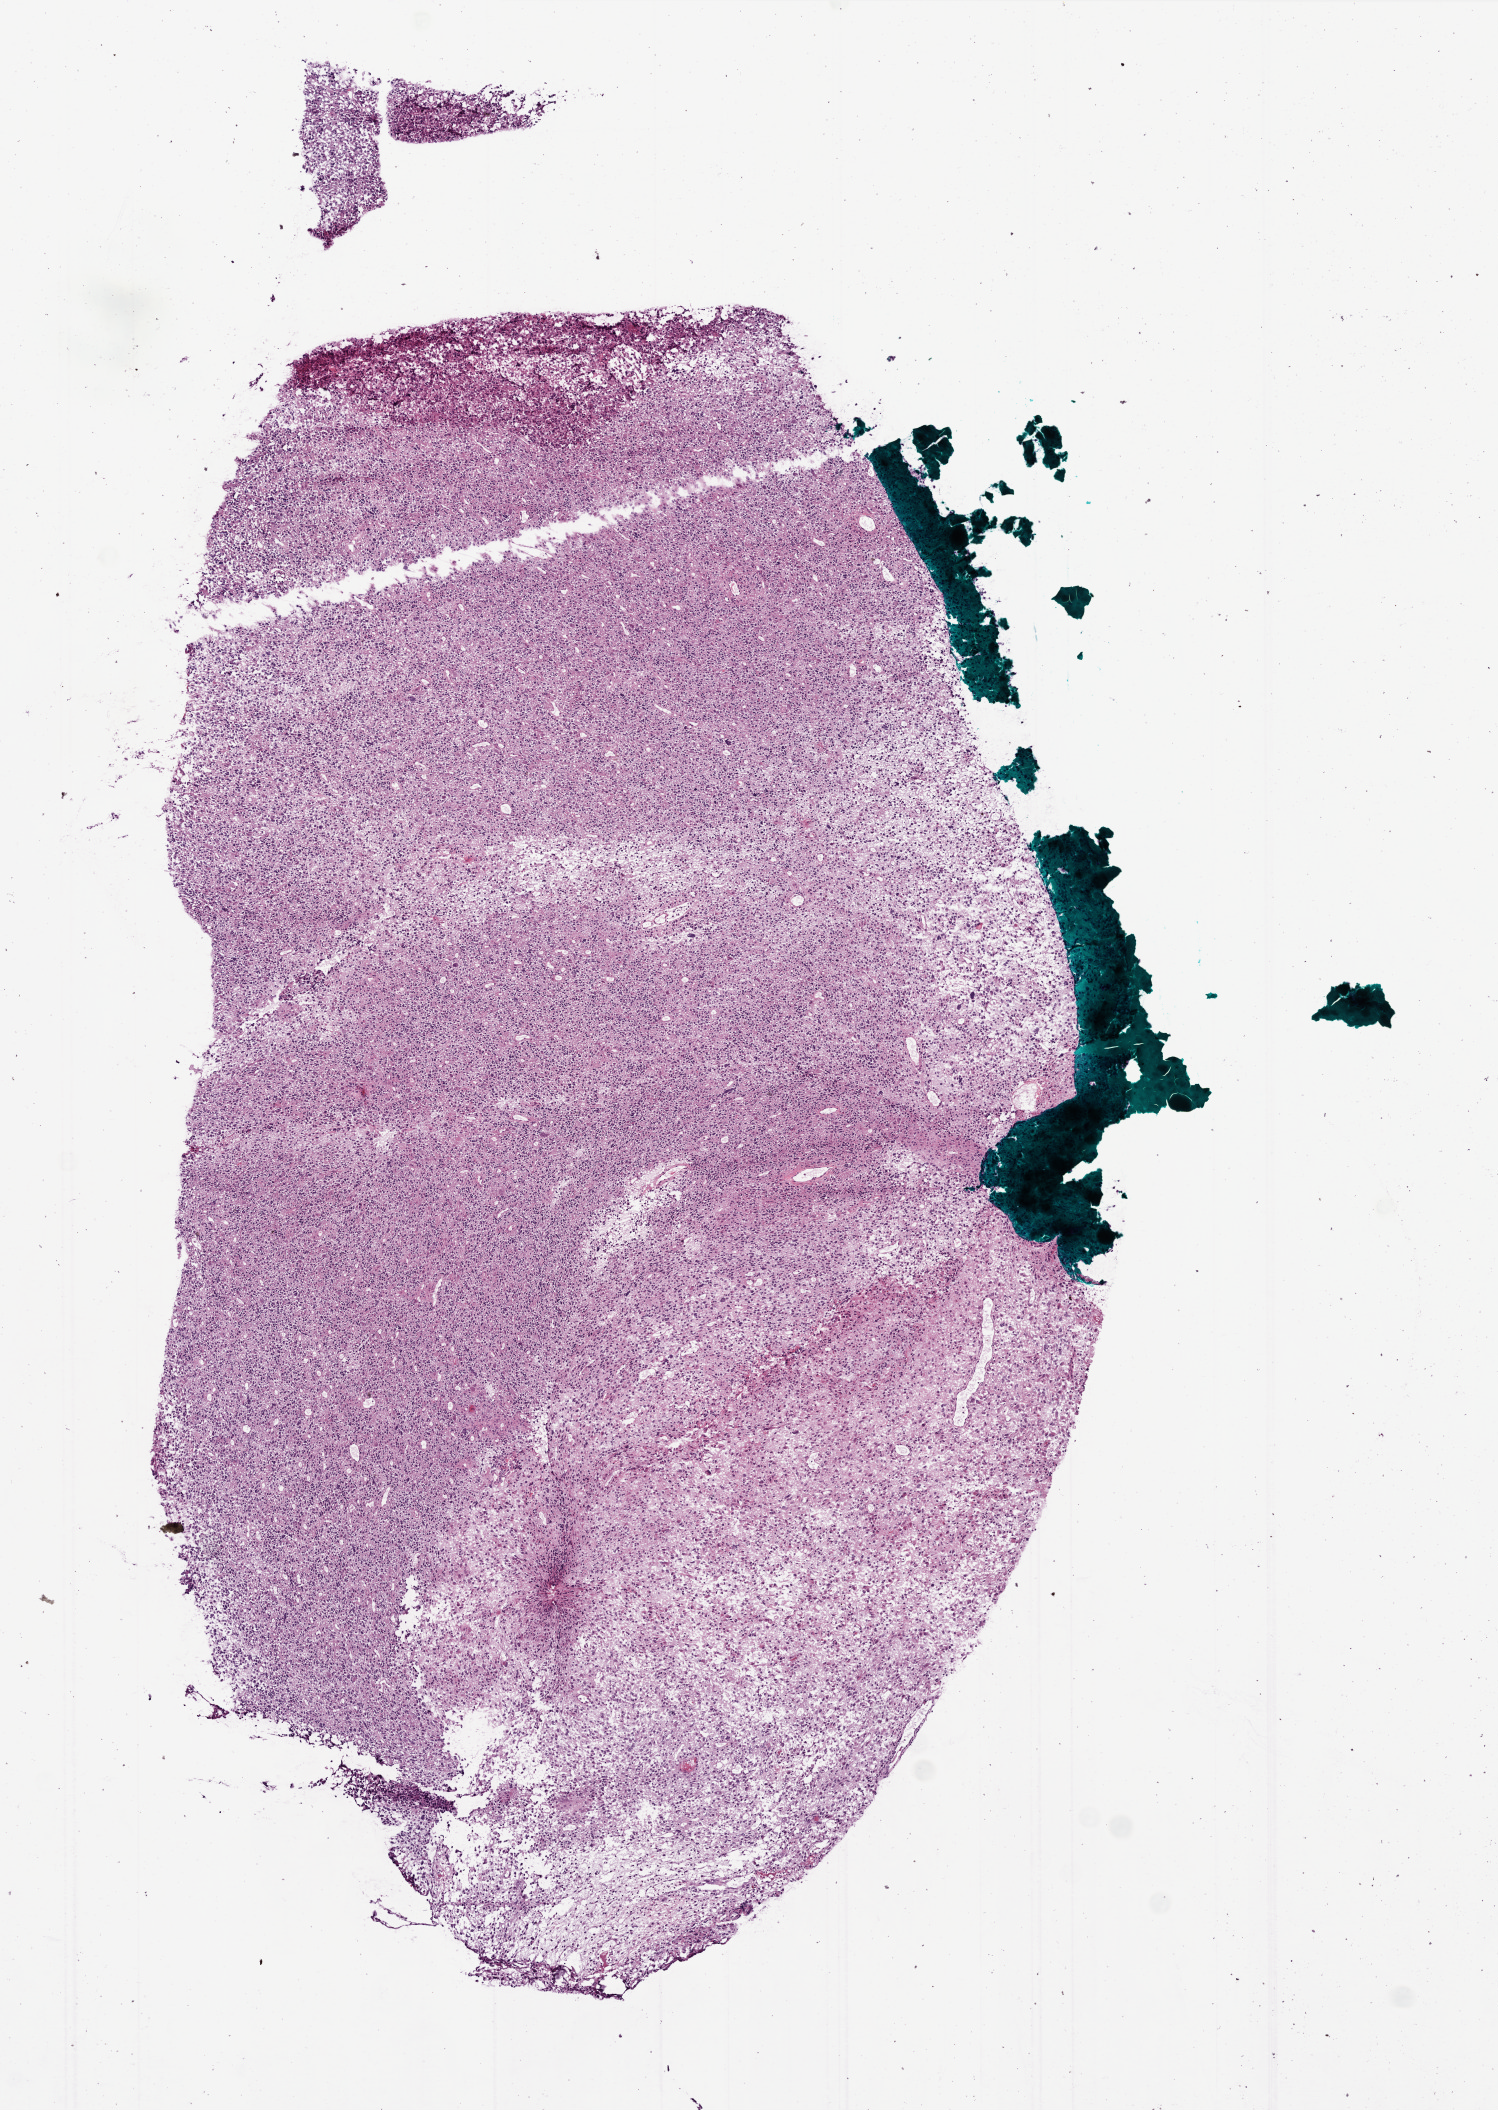
H&E whole-slide image — shown as a low-resolution overview of the whole scanned area (about 6.0 x 8.4 mm, from a 20x scan). Frozen section from the bottom of the tissue portion. Sample: primary tumour, brain. Male patient; age at initial diagnosis 14 years. Composition of this section per pathologist review: tumour cells 95%, tumour nuclei 100%, normal cells 0%, stromal cells 0%, necrosis 5%.
Pathologic diagnosis: Glioblastoma.